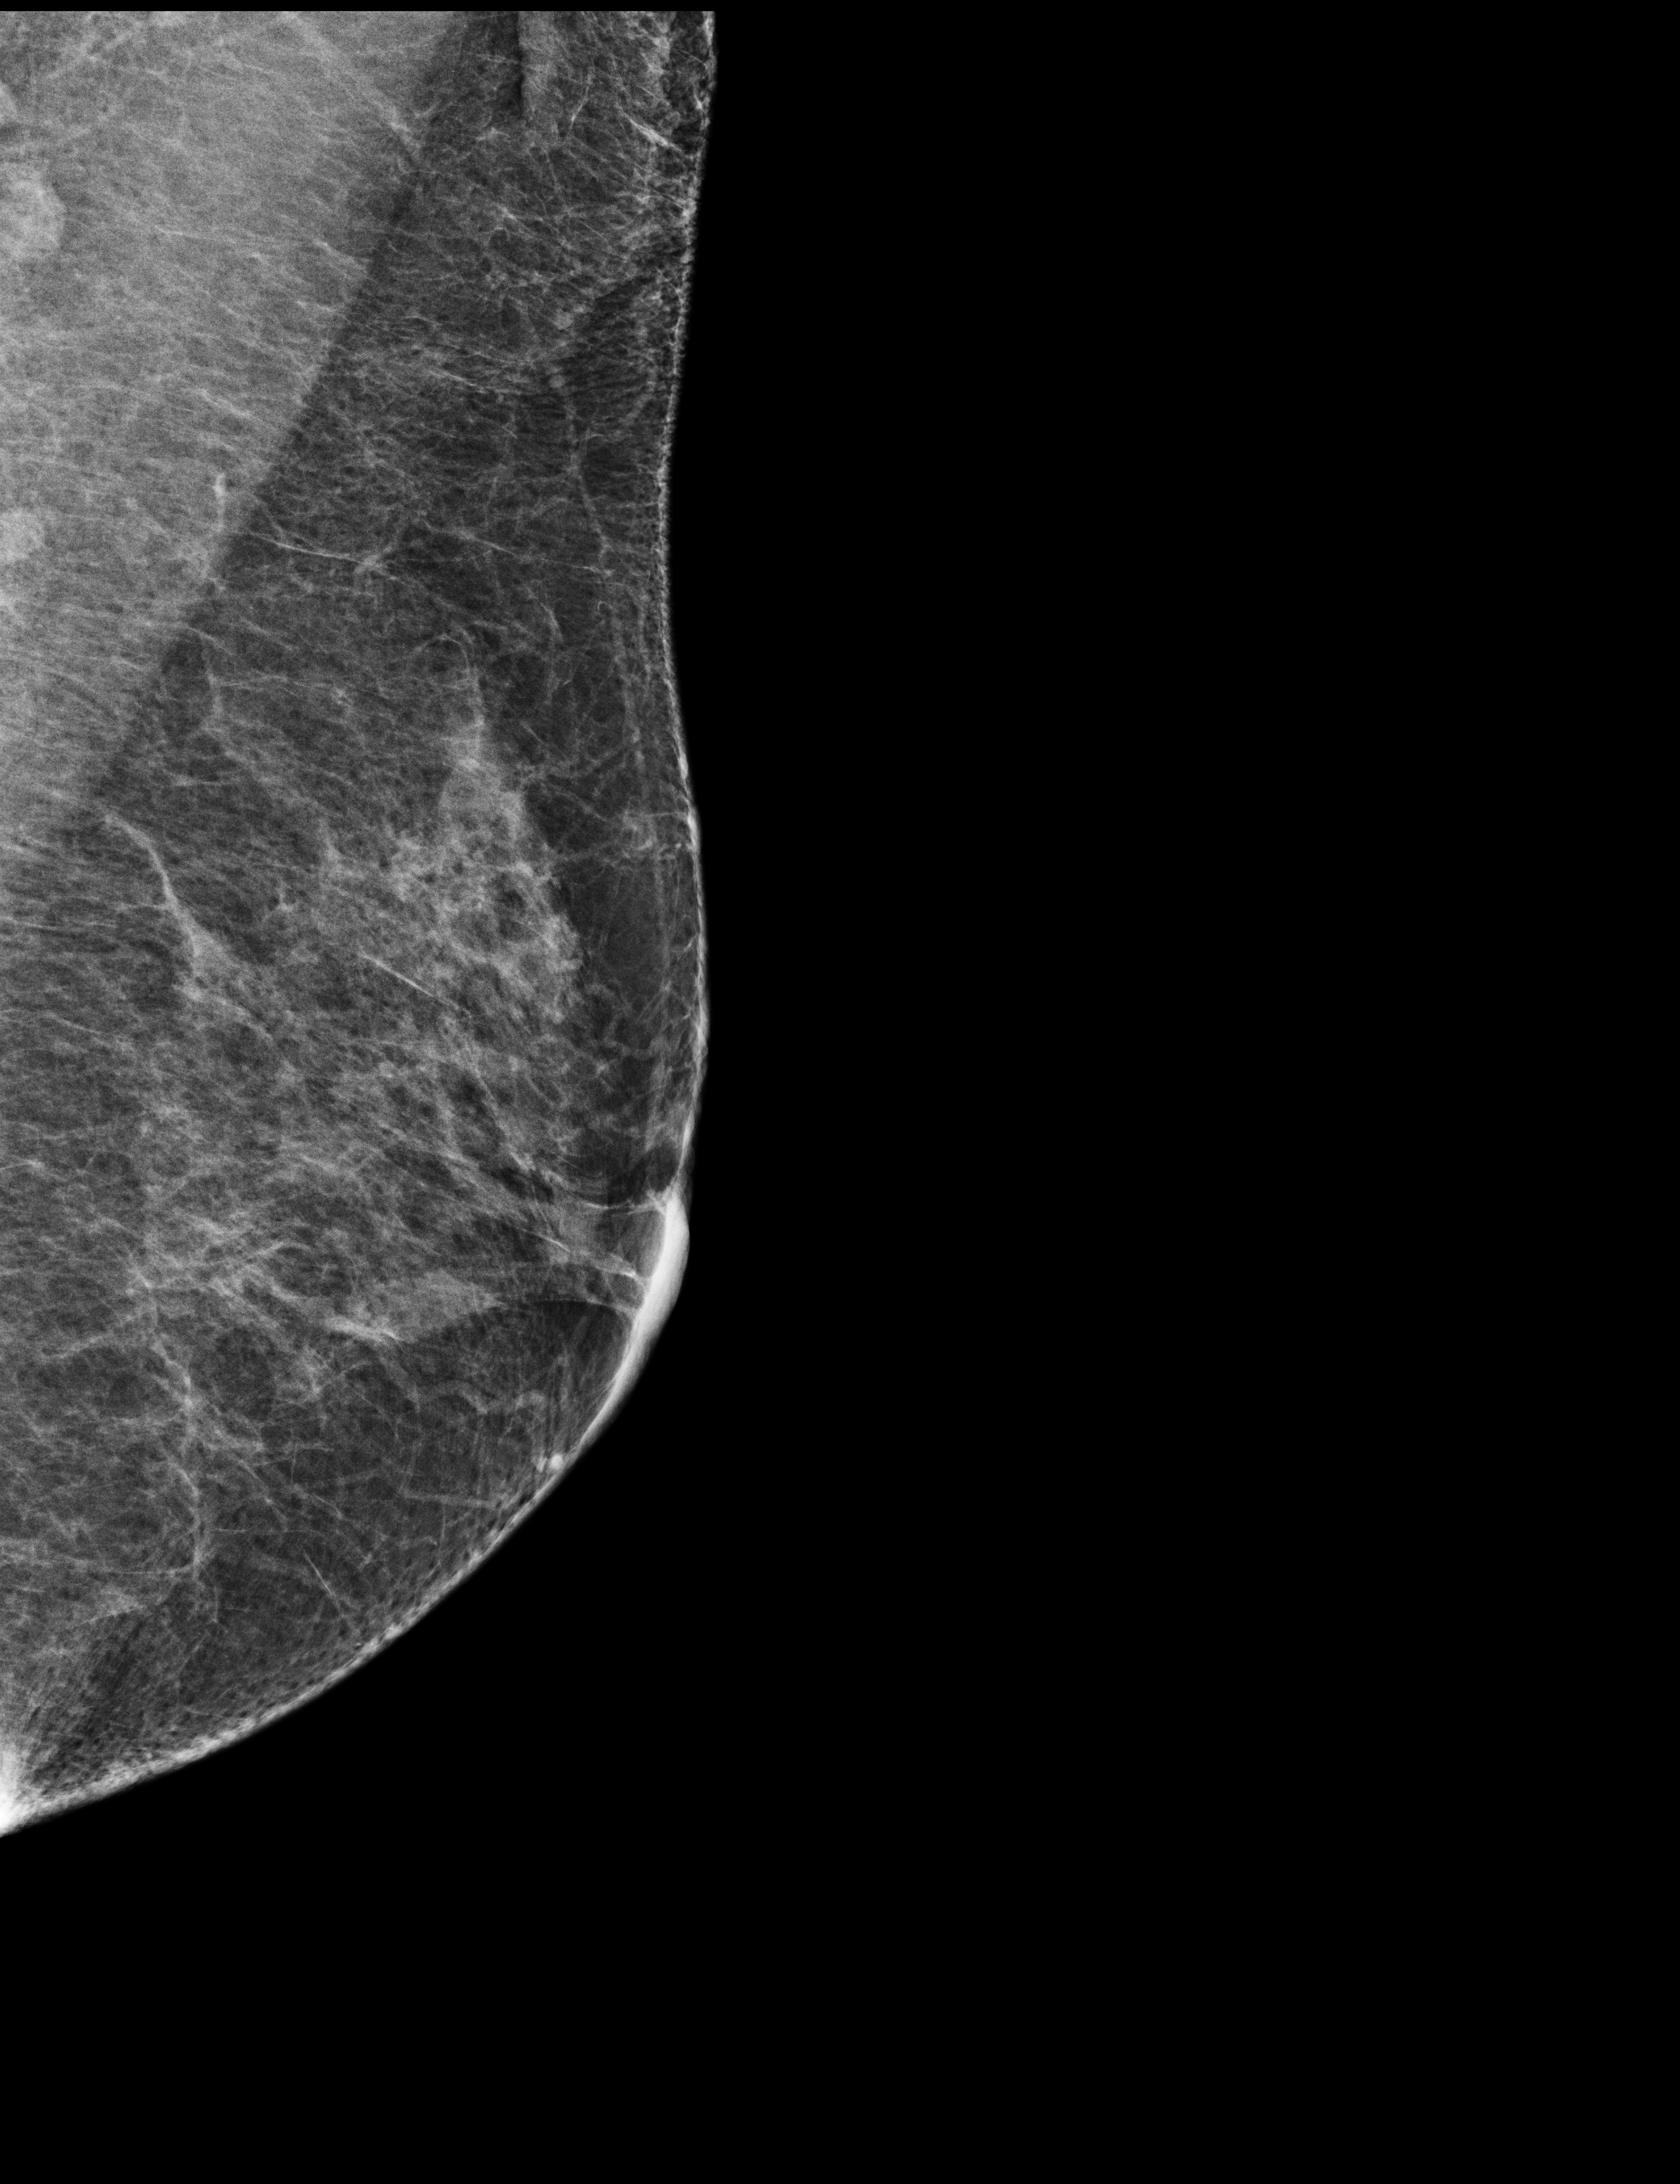
Full-field digital mammogram (FFDM), left breast, MLO view, annual screening mammography examination, system: Selenia Dimensions. Patient aged 72 years (female).
Breast density at the screening exam (both breasts): heterogeneously dense (BI-RADS density category c). Final BI-RADS assessment for this screening round (tomosynthesis exam, both breasts): category 1. Recall: no recall after this screen.